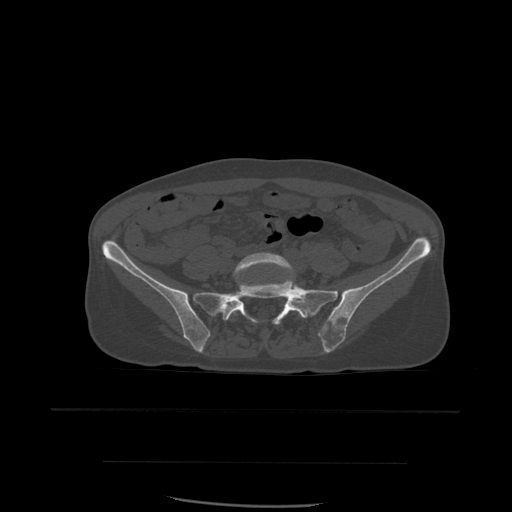
CT including the spine, one axial slice. Position 134 of 574 along the scan axis. Bone window (W 1800 / L 400 HU). 1.25 mm slice thickness. 512 × 512 image matrix, field of view 392 × 392 mm. Patient age 48 years. Case-level facts recorded for this patient, not image findings: primary cancer: lung.
Structures marked on this image (semi-automatic segmentation, software-assisted and operator-edited):
- L5 vertebra: bounding box <229,252,304,318> (left, top, right, bottom; pixels)